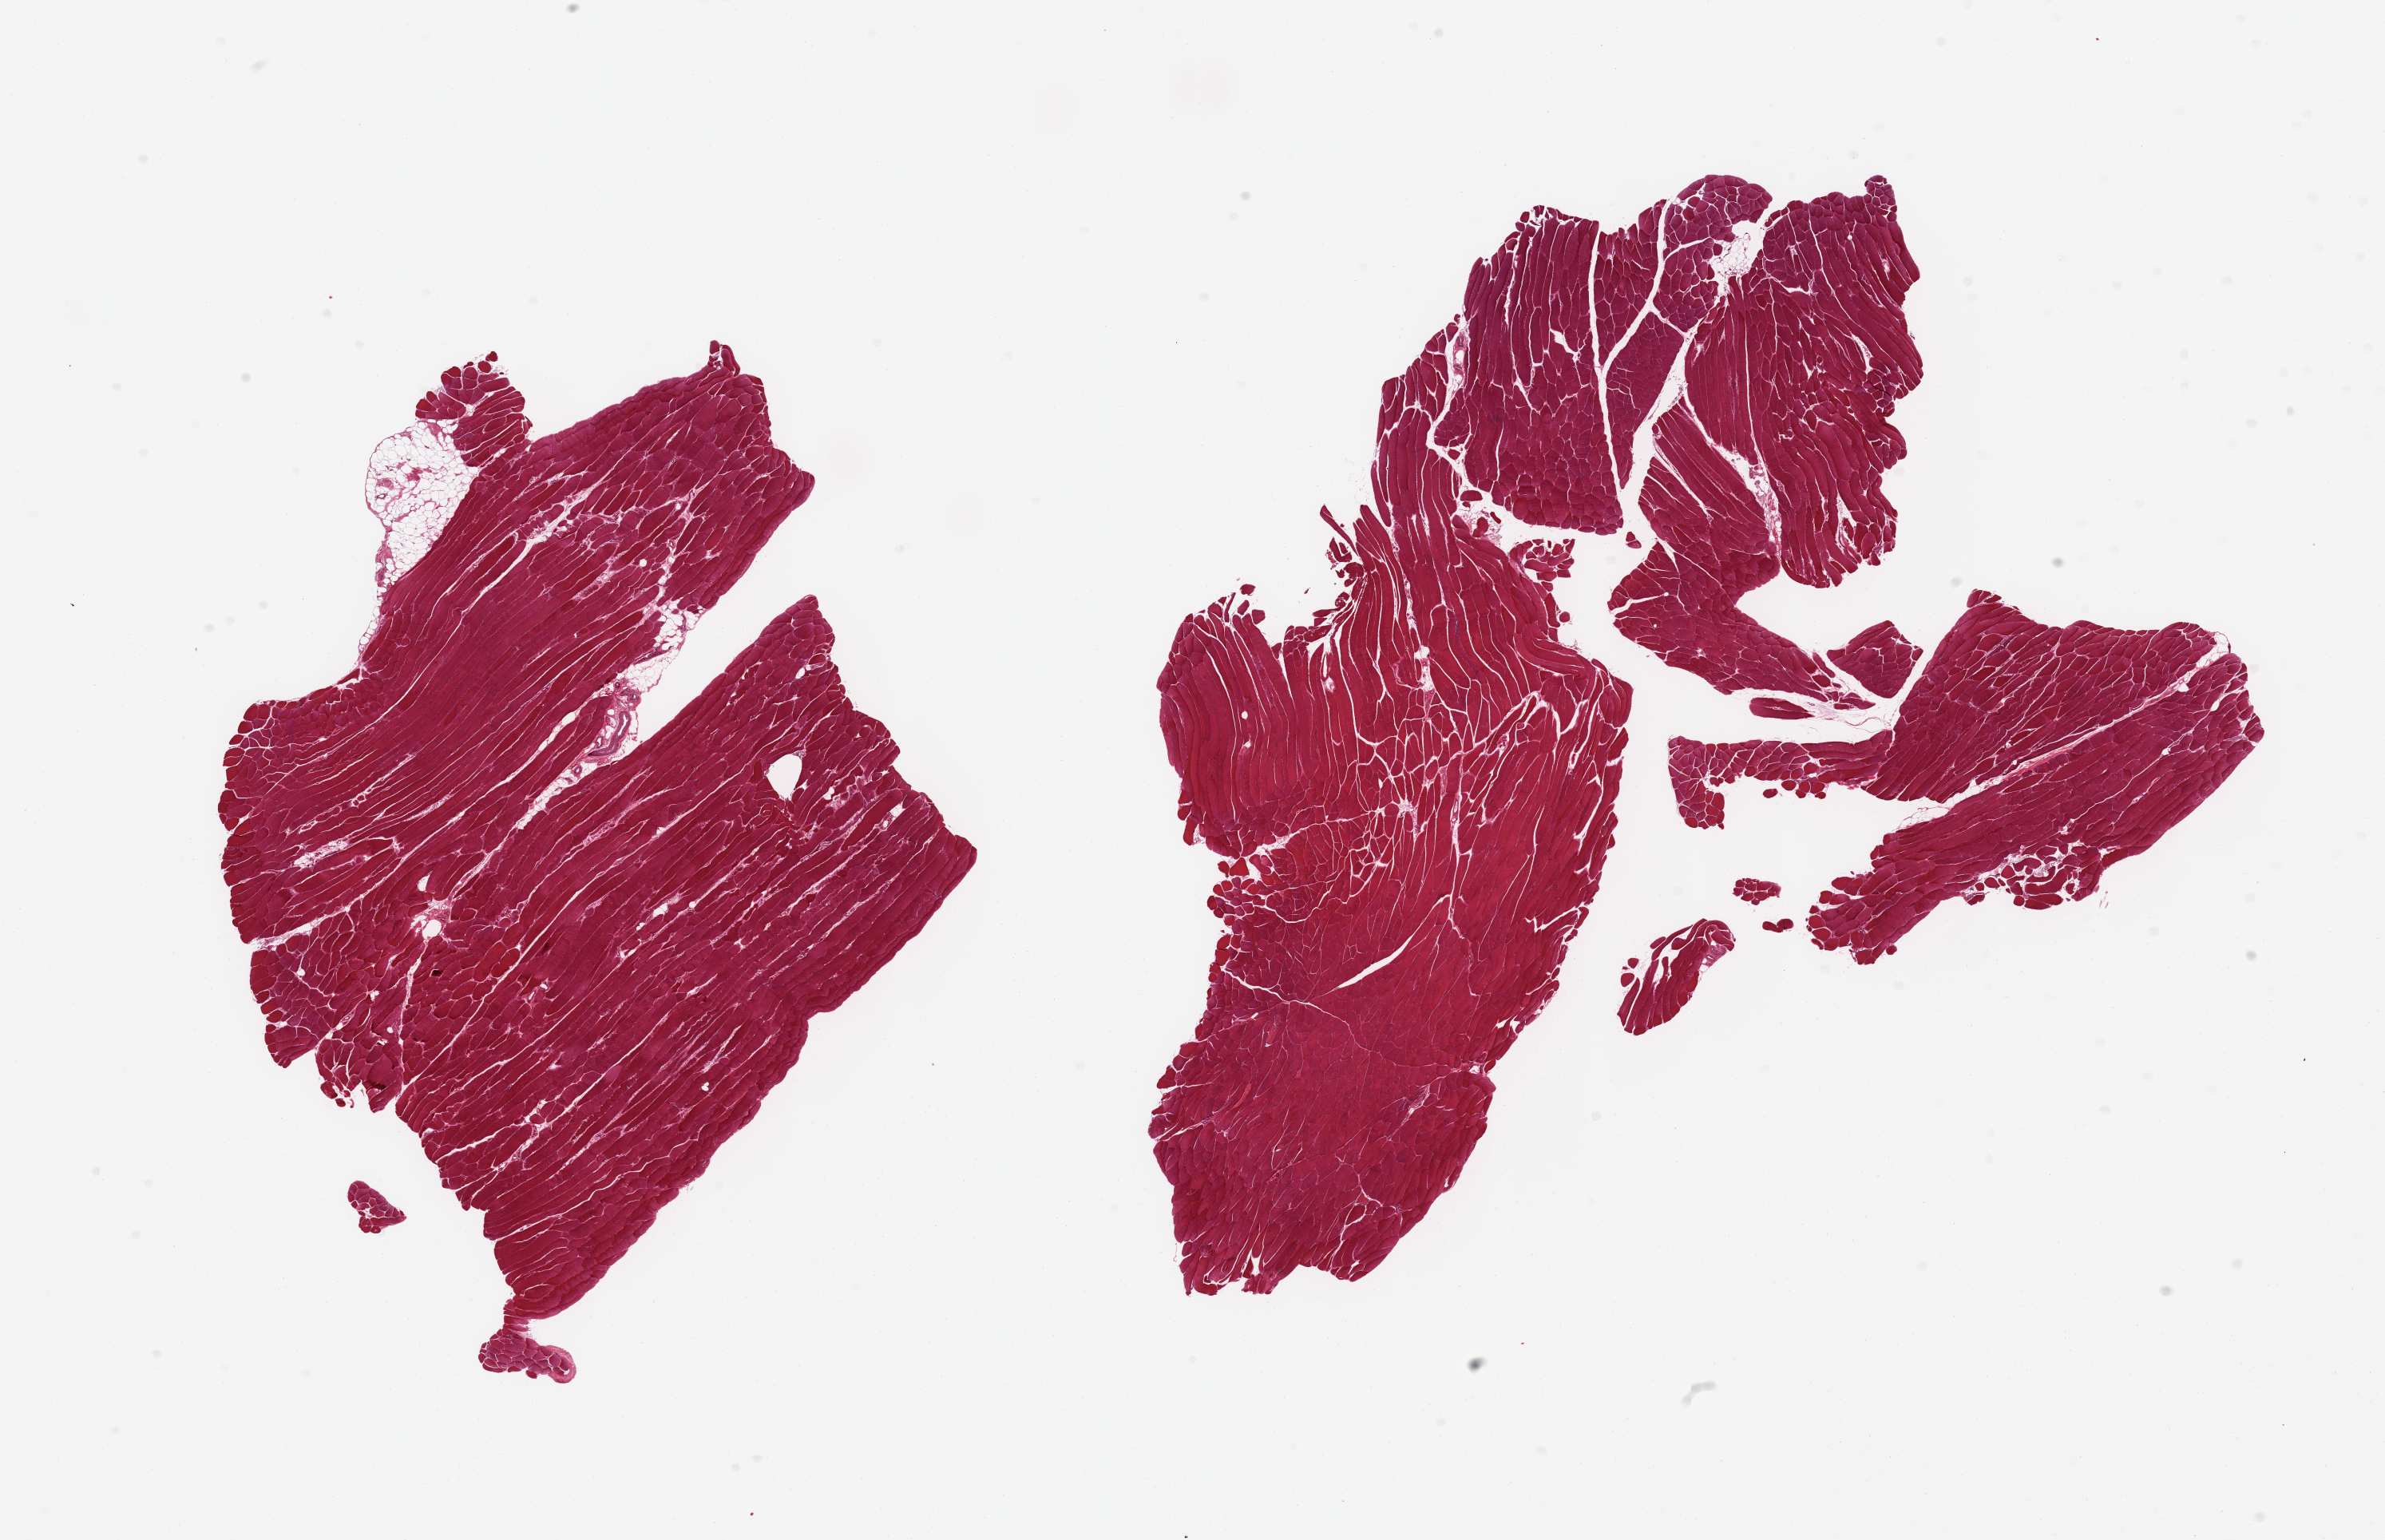
Haematoxylin and eosin whole-slide image, brightfield — whole scanned area (about 23.6 x 15.3 mm, acquisition: 20x scan) shown as a low-resolution overview; PAXgene-fixed, paraffin-embedded tissue; sampled site (target tissue): skeletal muscle; tissue donor sample. Donor: male.
Reviewer comment on this tissue sample: 2 pieces, ~5-10% adherent / interstitial fat.